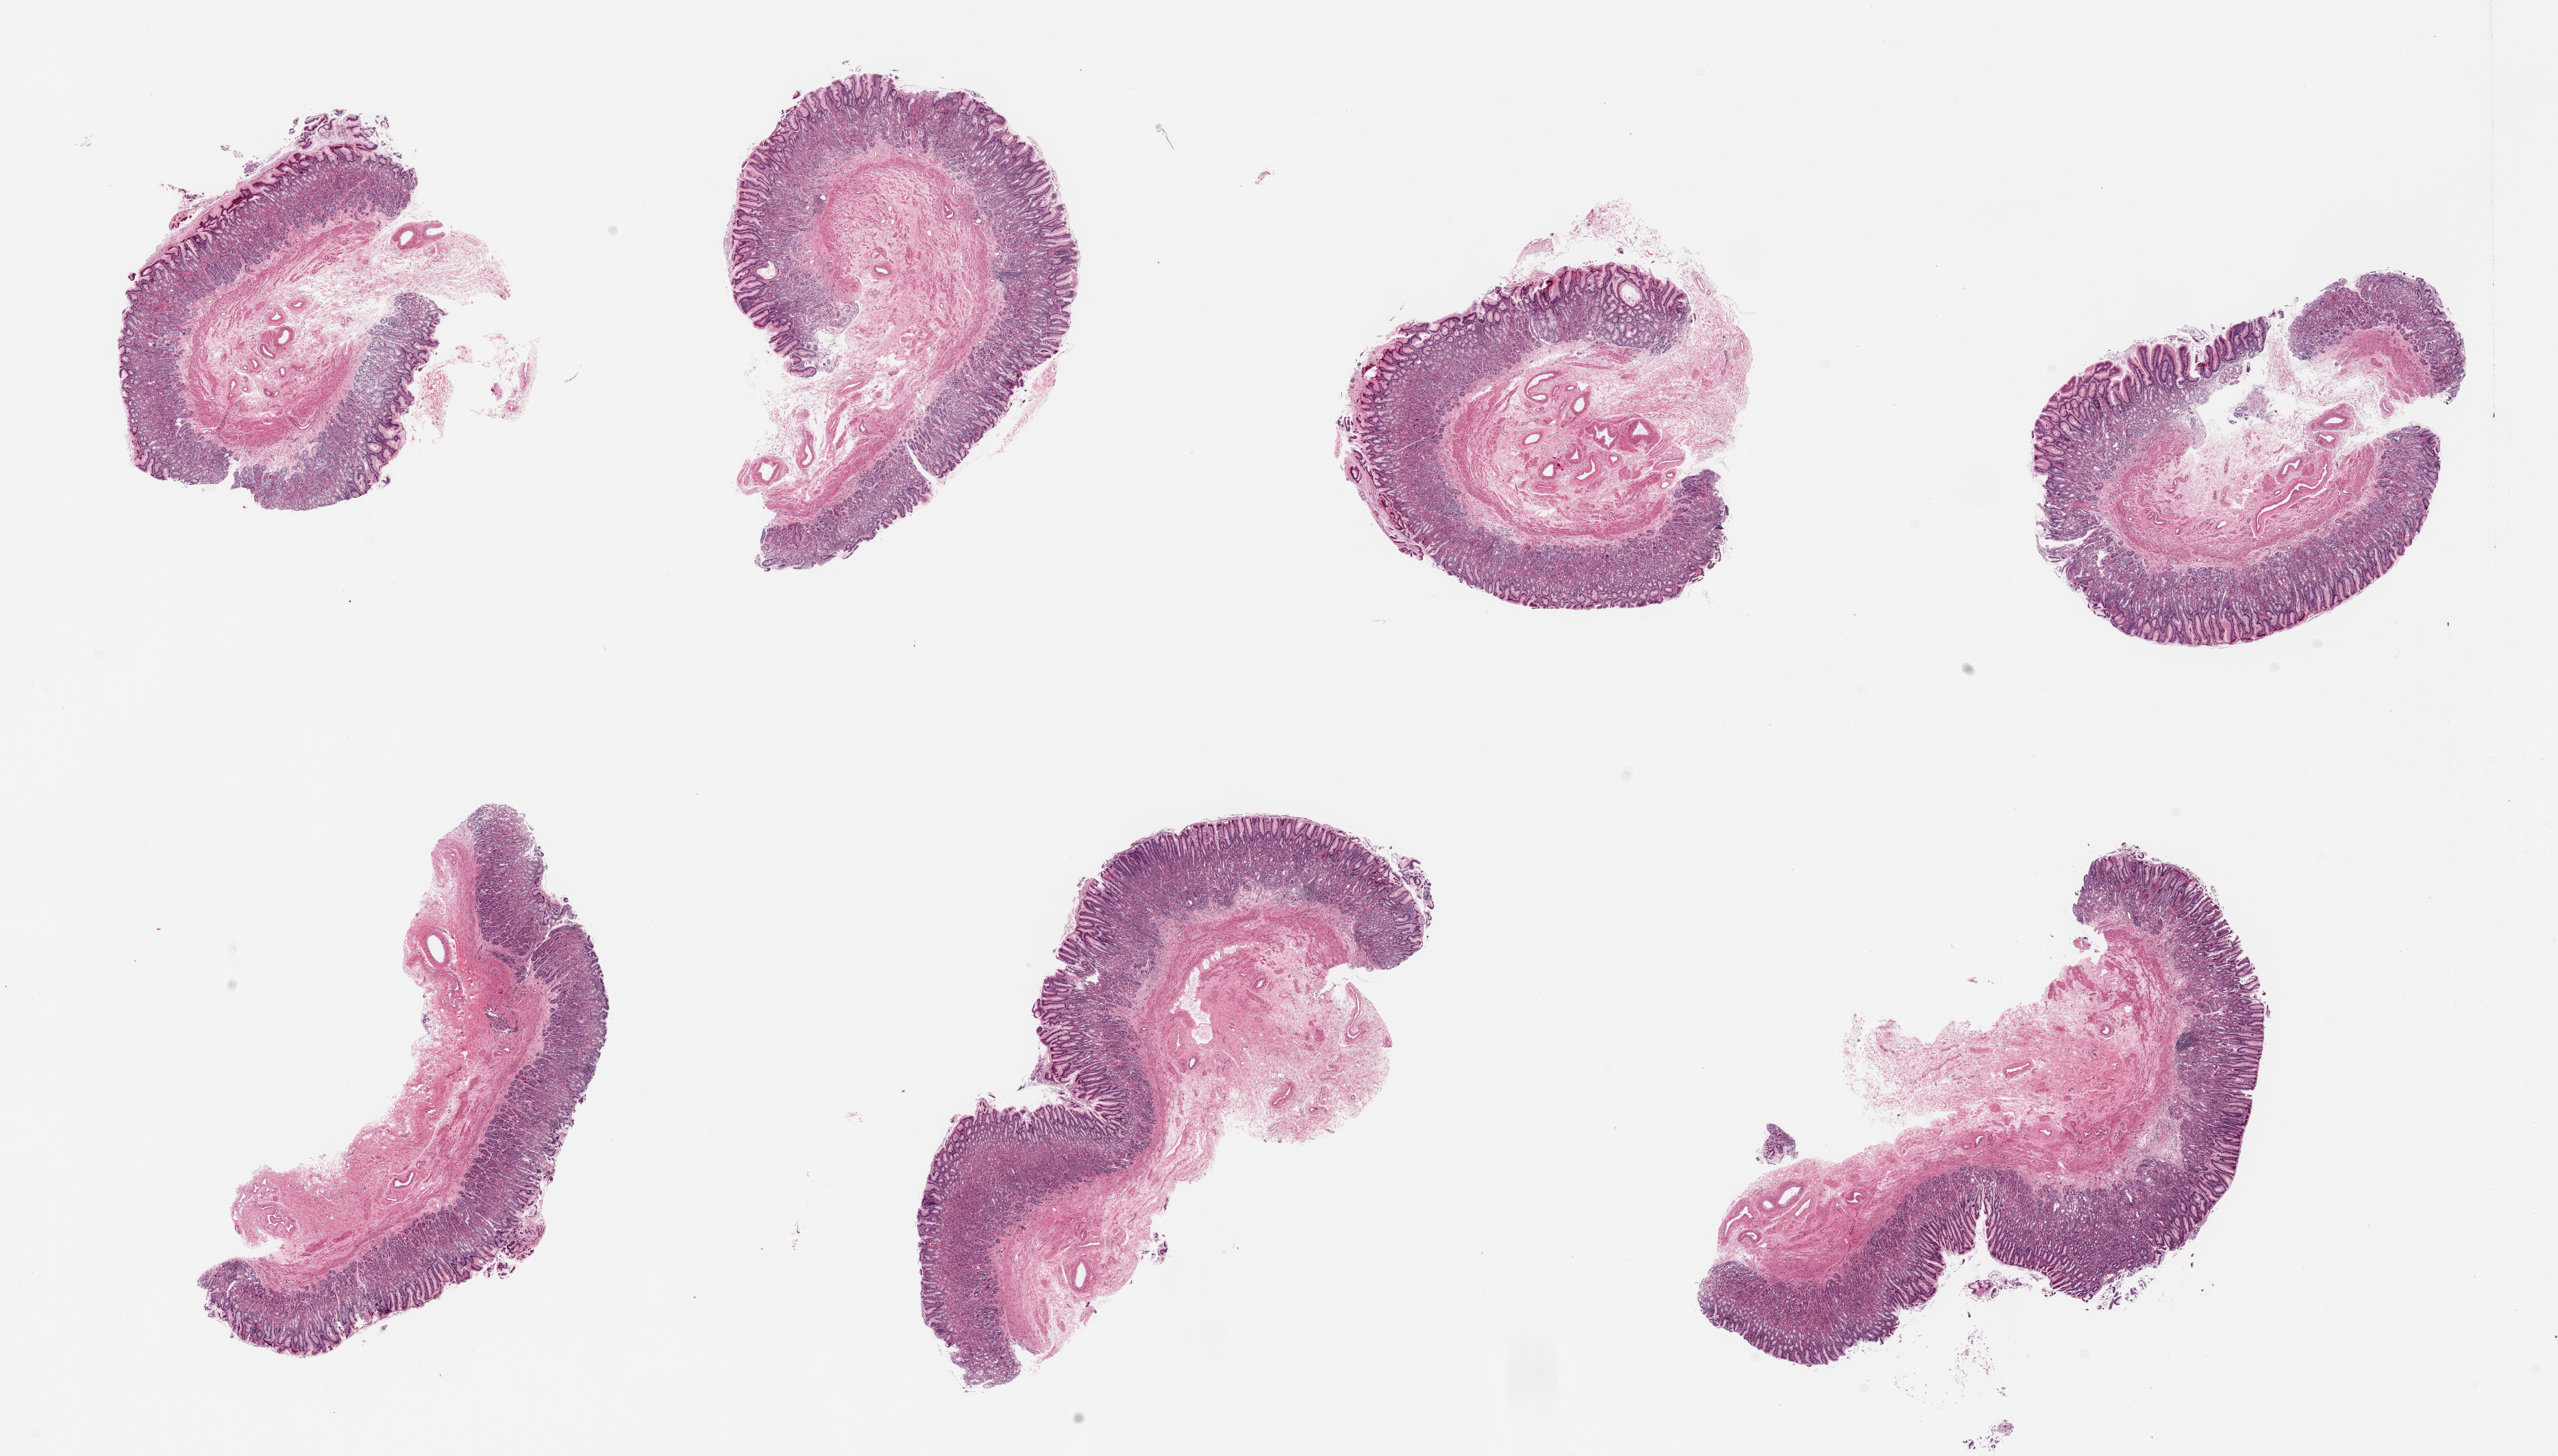
Hematoxylin and eosin (H&E) whole-slide image, brightfield — a low-resolution overview of the entire scanned area, about 29.5 x 16.8 mm (from a 20x scan). Donor sex: female.
- specimen: PAXgene-fixed paraffin-embedded (PFPE) section; sampled site (target tissue): stomach; tissue donor sample